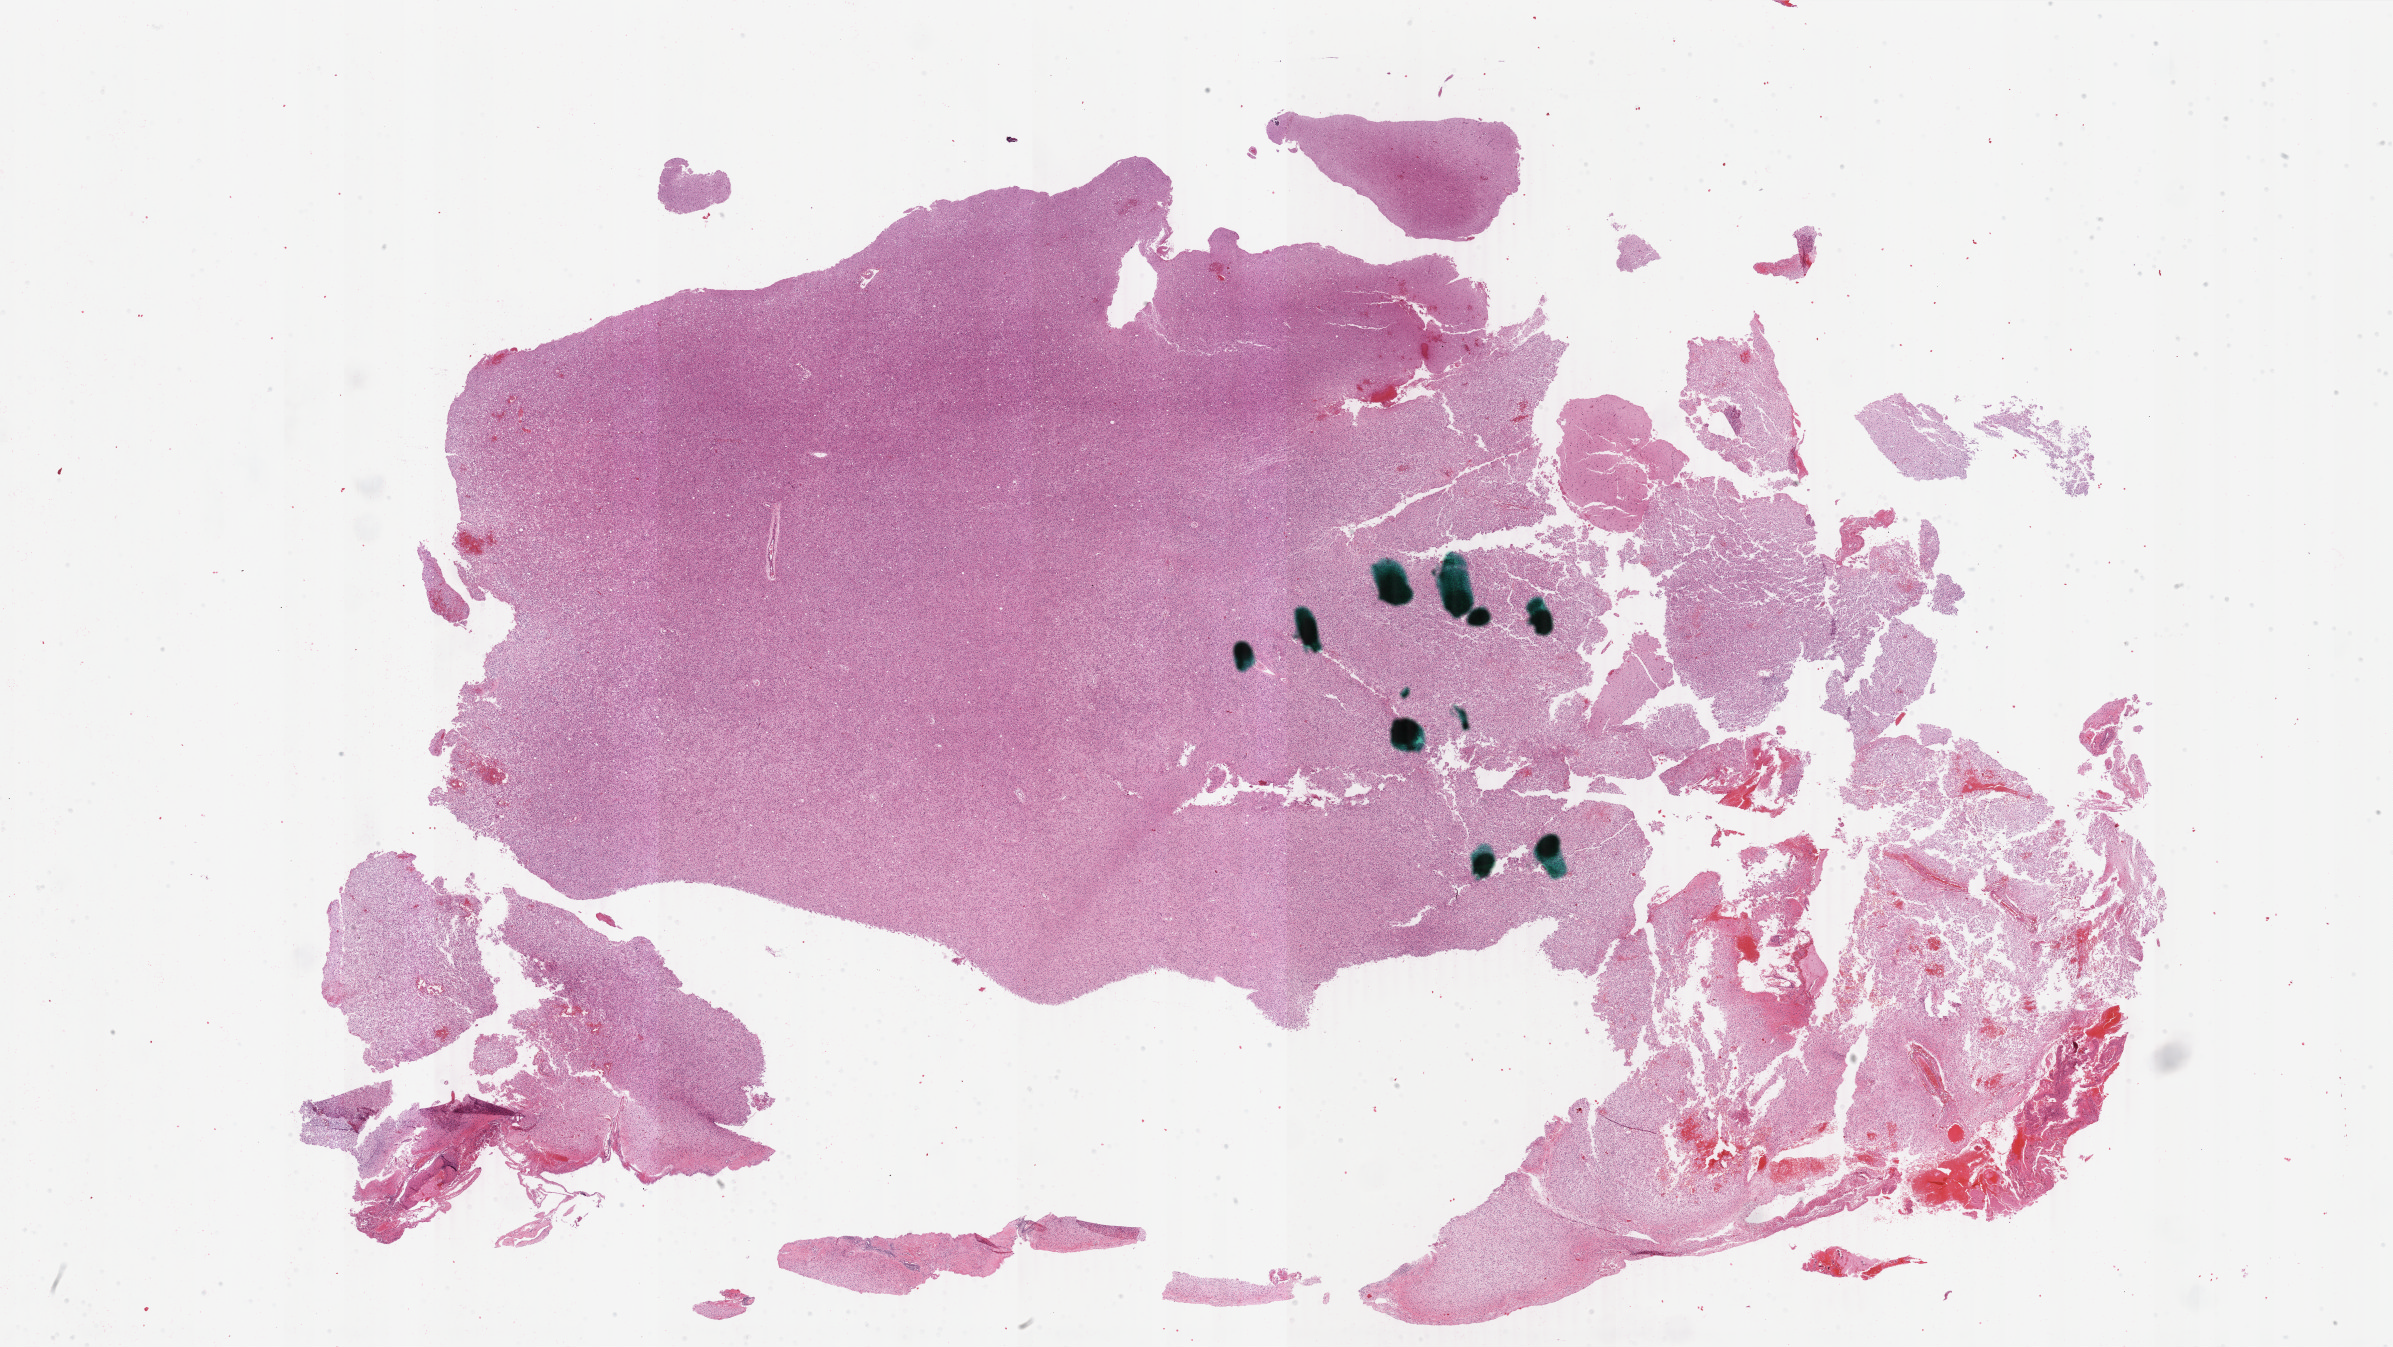
Whole-slide histology image, H&E-stained, shown as a low-resolution overview of the whole scanned area (about 38.1 x 21.4 mm). Formalin-fixed paraffin-embedded (FFPE) diagnostic section. Brain, primary tumour sample. Patient: female, age at initial diagnosis 43 years. Histologic grade: G3 (poorly differentiated).
Diagnosis: Astrocytoma, anaplastic (cerebrum). Laterality: right.